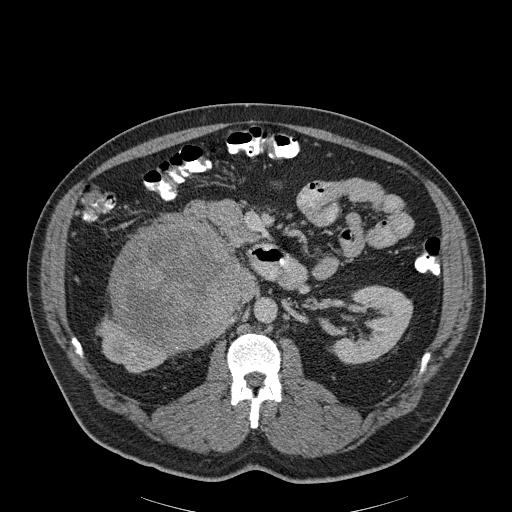
Contrast-enhanced abdominal CT, one axial slice. Slice 114 of 186 in the series (ordered by position). Reconstruction kernel B30f. 120 kVp. Soft-tissue window (W 400 / L 40 HU). 512 × 512 image matrix. Male patient, age 56 years. Case-level facts recorded for this patient, not image findings: diagnosis: adrenocortical carcinoma; tumour side: right adrenal; tumour size at pathology: 18 cm.
Annotated regions visible in this slice (semi-automatic segmentation, software-assisted and operator-edited):
- mass: bounding box (x1, y1, x2, y2) in pixels: (111, 215, 240, 348)